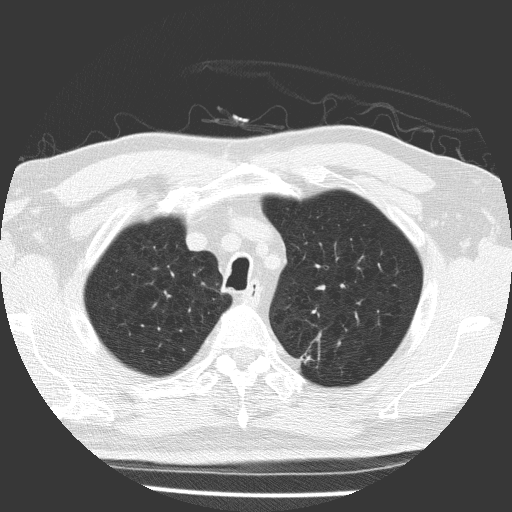
Low-dose screening chest CT, one axial slice; slice 137 of 169 in the series (ordered by position); reconstruction kernel FC51; 120 kVp; lung window (W 1500 / L -600 HU); 2 mm slice thickness; 512 × 512 image matrix, field of view 323 × 323 mm.
Structures marked on this image (expert manual segmentation):
- lesion 1 (tumor, upper lobe of left lung): bounding box (x1, y1, x2, y2) in pixels: (300, 353, 314, 364)